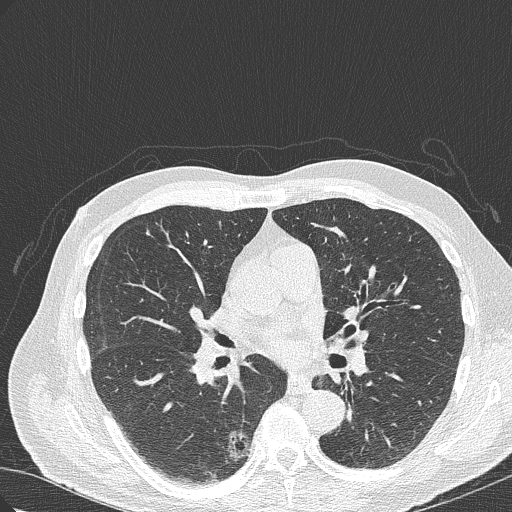
Low-dose screening chest CT, axial slice; first (baseline) screen; lung window (W 1500 / L -600 HU); lung (sharp) reconstruction kernel (B50f). Male participant, aged 70 years at enrolment. Current smoker at enrolment.
- Lesion marked by an expert reader, box from (x=198, y=420) to (x=261, y=480) px.
- The screening reader recorded 4 non-calcified nodules or masses ≥4 mm on this exam; which of them this box marks is not recorded.
- Official screen result: positive, change unspecified: nodule(s) >= 4 mm or enlarging nodule(s), mass(es), or other non-specific abnormalities suspicious for lung cancer.
- Lung cancer was diagnosed 978 days after this screen: bronchiolo-alveolar adenocarcinoma, NOS, right lower lobe, poorly differentiated (G3), stage IB (AJCC 6th edition), 30 mm at pathology.